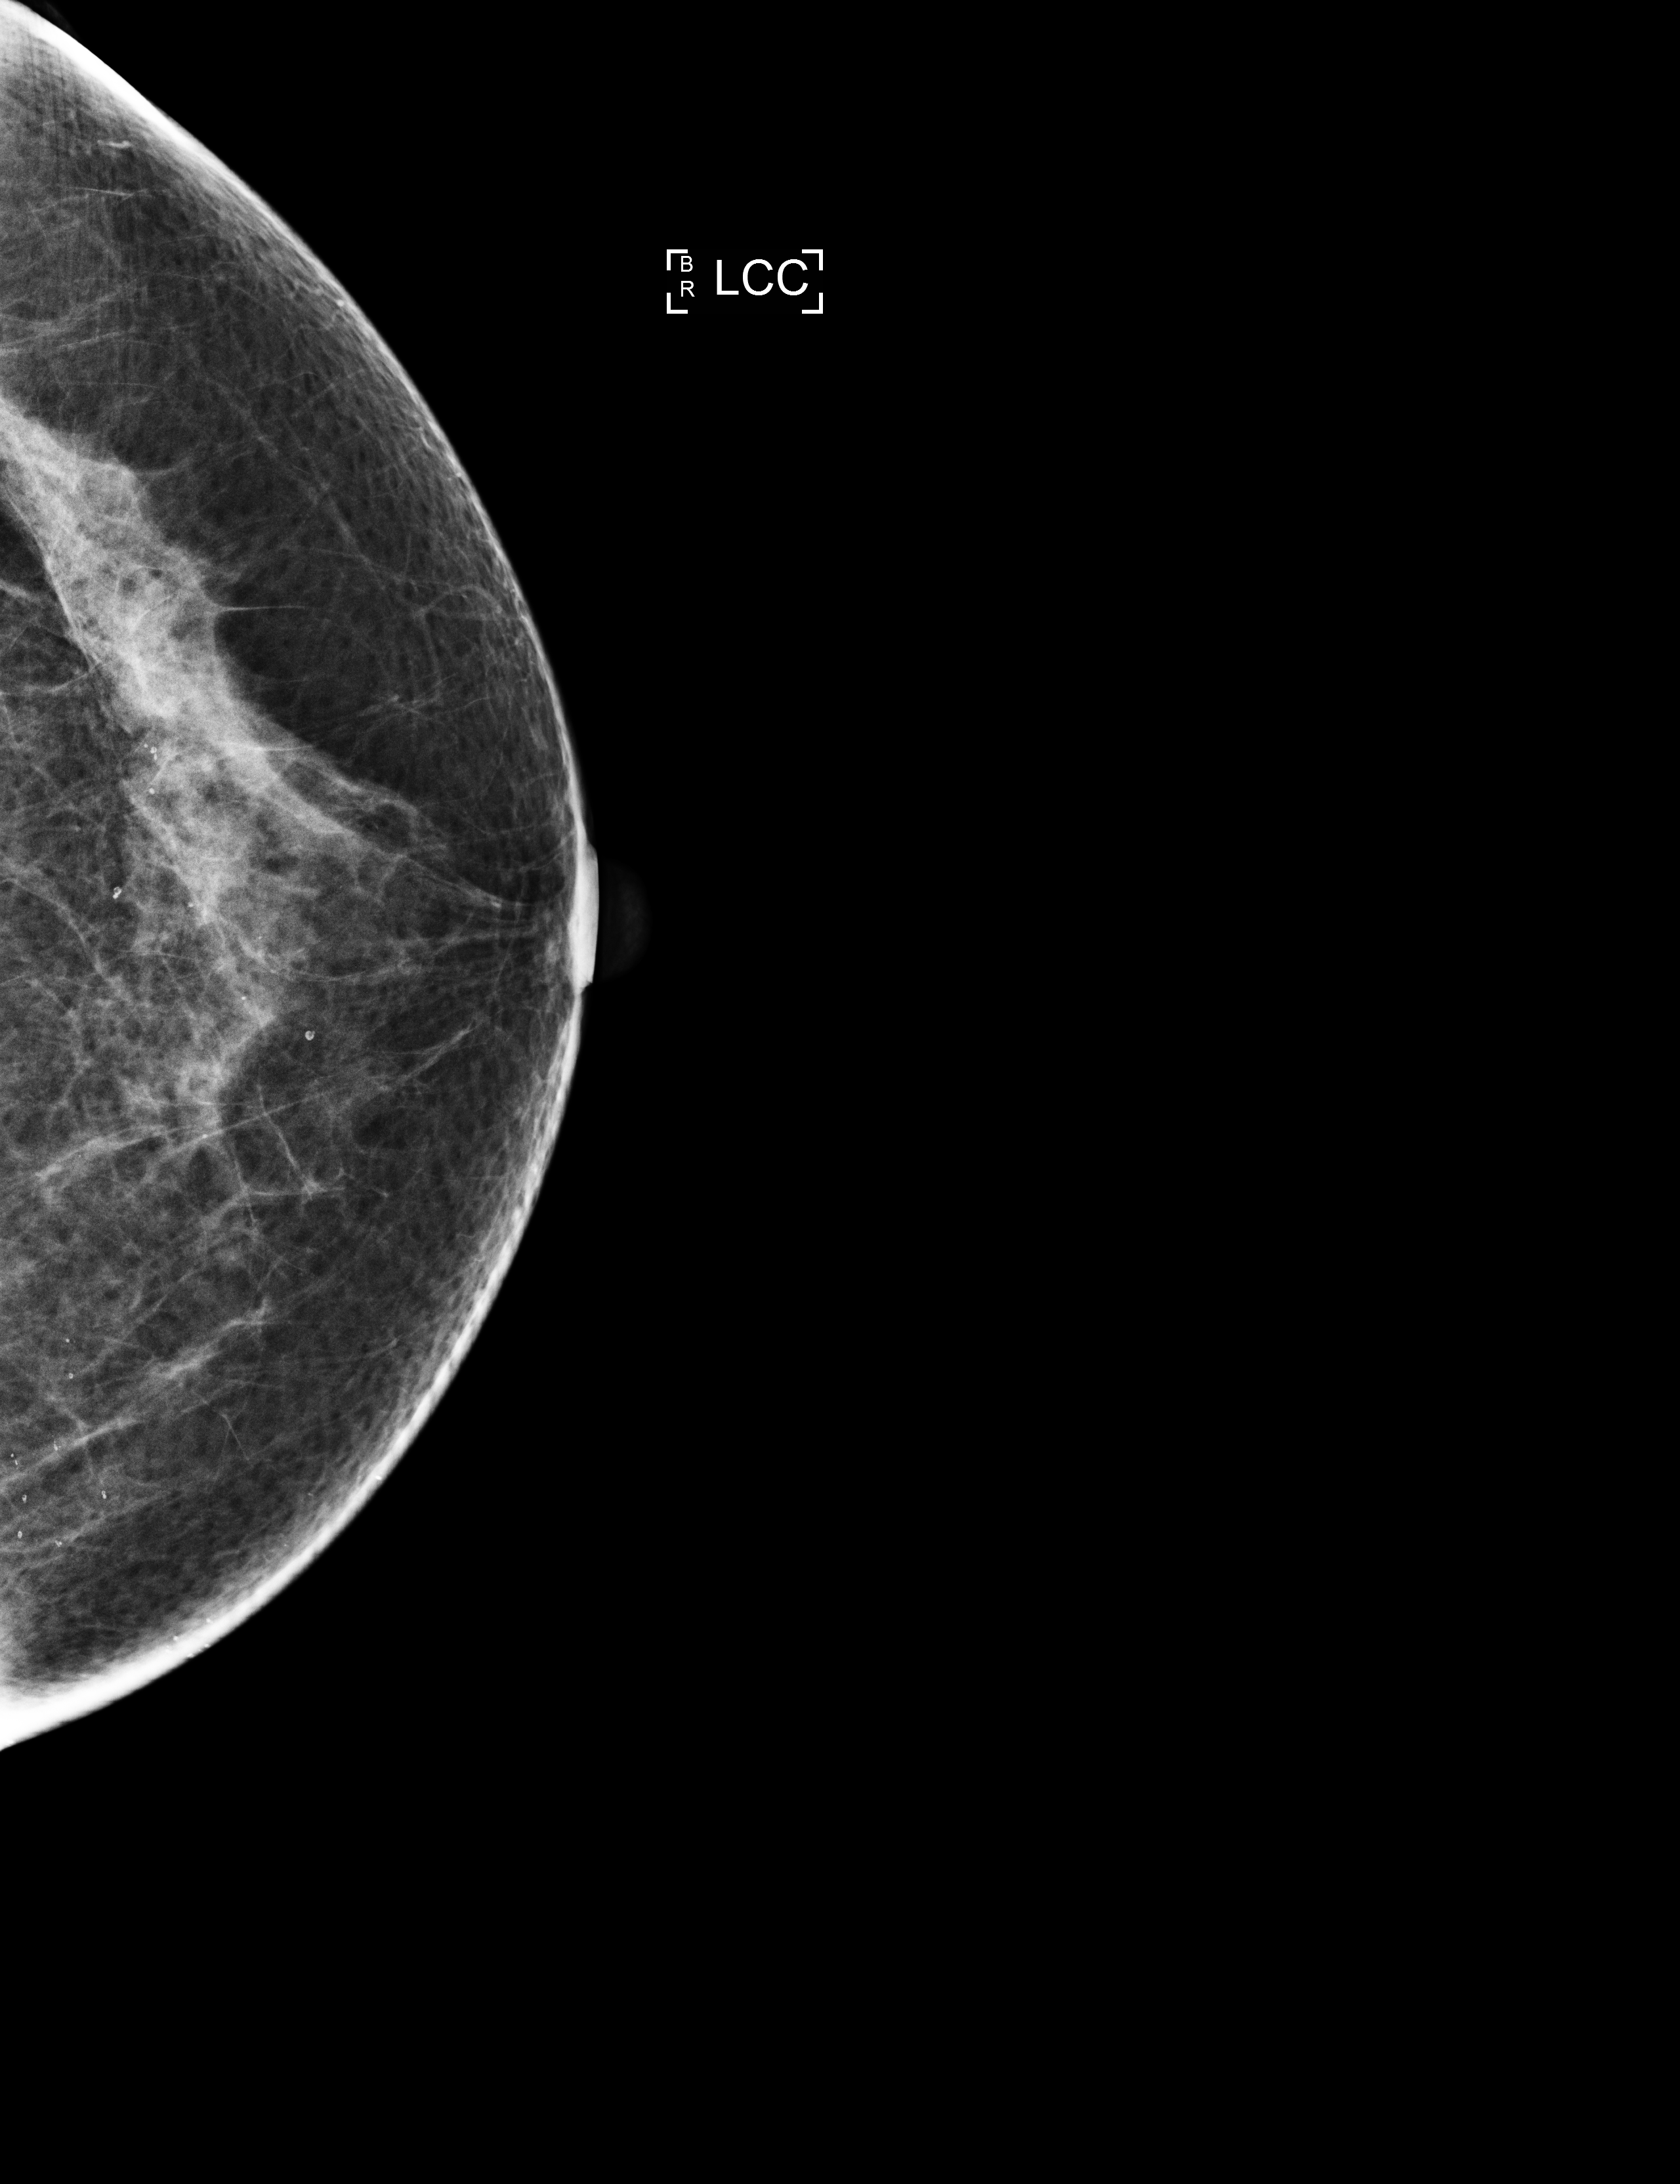
Annual screening mammography examination. Patient aged 69 years (female).
Image type: full-field digital mammogram. Breast: left. Projection: craniocaudal (CC) view.